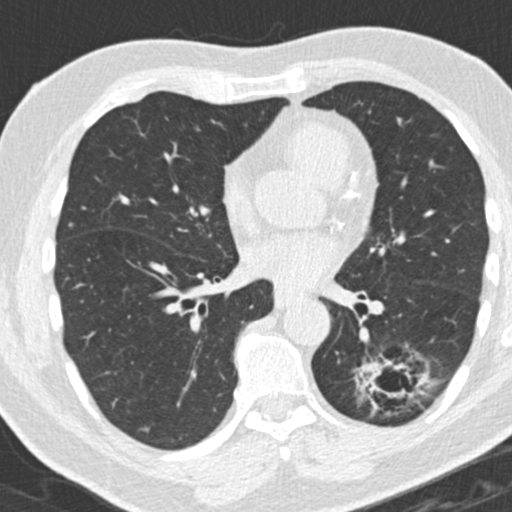
Low-dose screening chest CT, axial slice. Third annual screen. Lung window (W 1500 / L -600 HU). 2 mm slice thickness. Slice 89 of 180 in the series. 512 × 512 image matrix. Male, age 66 years at enrolment. Former smoker at enrolment.
• Expert-annotated lung lesion, bounding box (x1, y1, x2, y2) in pixels: (356, 349, 426, 428).
• Screening reader's record for this exam (one nodule recorded; not confirmed to be the boxed lesion): non-calcified nodule or mass ≥4 mm, left lower lobe, 31 × 24 mm, spiculated (stellate) margins, pre-existing on the prior screen: yes; interval growth: yes.
• Lung cancer was diagnosed 56 days after this screen: adenocarcinoma, NOS, left lower lobe, poorly differentiated (G3), stage IB (AJCC 6th edition), 38 mm at pathology.